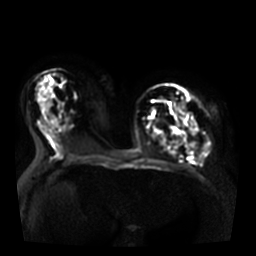
Breast MRI, one axial slice. Slice 20 of 36 in the series (ordered by position). Diffusion-weighted series; image 2 of 4 stored at this slice position (different b-values; order by instance number). 3 T. 5 mm slice thickness. 256 × 256 image matrix, field of view 350 × 350 mm. Female patient.
Annotated regions visible in this slice (expert manual segmentation):
- tumour on diffusion-weighted imaging: box from (x=178, y=101) to (x=185, y=110) px